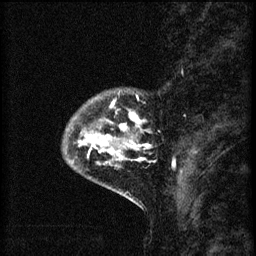
Breast MRI (dynamic contrast-enhanced), one sagittal slice; slice 12 of 60 in the series (ordered by position); 3 images stored at this slice position (order not interpretable as contrast timing); 1.5 T; TE 4.2 ms, TR 8.2 ms; 256 × 256 image matrix, field of view 180 × 180 mm. Patient: female, 41 years.
Annotated regions visible in this slice (semi-automatic segmentation, software-assisted and operator-edited):
- analysis volume of interest (the breast-tissue region the enhancement analysis was run in; not a lesion): box from (x=63, y=90) to (x=151, y=175) px
- tumour enhancement mask (voxels above the 70 % enhancement threshold inside the analysis volume of interest): (x=78, y=104)–(x=151, y=165)